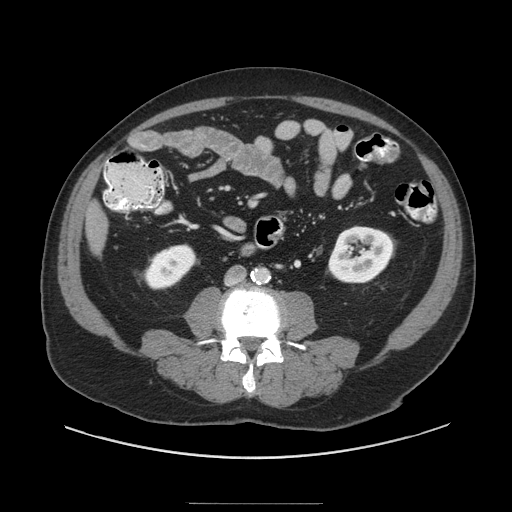
Contrast-enhanced abdominal CT (liver protocol), one axial slice. Reconstruction kernel STANDARD. 140 kVp. Soft-tissue window (W 400 / L 40 HU). 2.5 mm slice thickness. 512 × 512 image matrix, field of view 440 × 440 mm. Case-level facts recorded for this patient, not image findings: diagnosis: hepatocellular carcinoma (patient treated with transarterial chemoembolisation; whether this scan precedes or follows treatment is not stated here); TNM stage (as recorded): Stage-I; Child-Pugh class: A; tumour differentiation: well differentiated.
Annotated regions visible in this slice (semi-automatic segmentation, software-assisted and operator-edited):
- liver parenchyma outside the tumour (the mass and vessels are separate outlines, so this box may not span the whole liver): bounding box <86,202,108,252> (left, top, right, bottom; pixels)